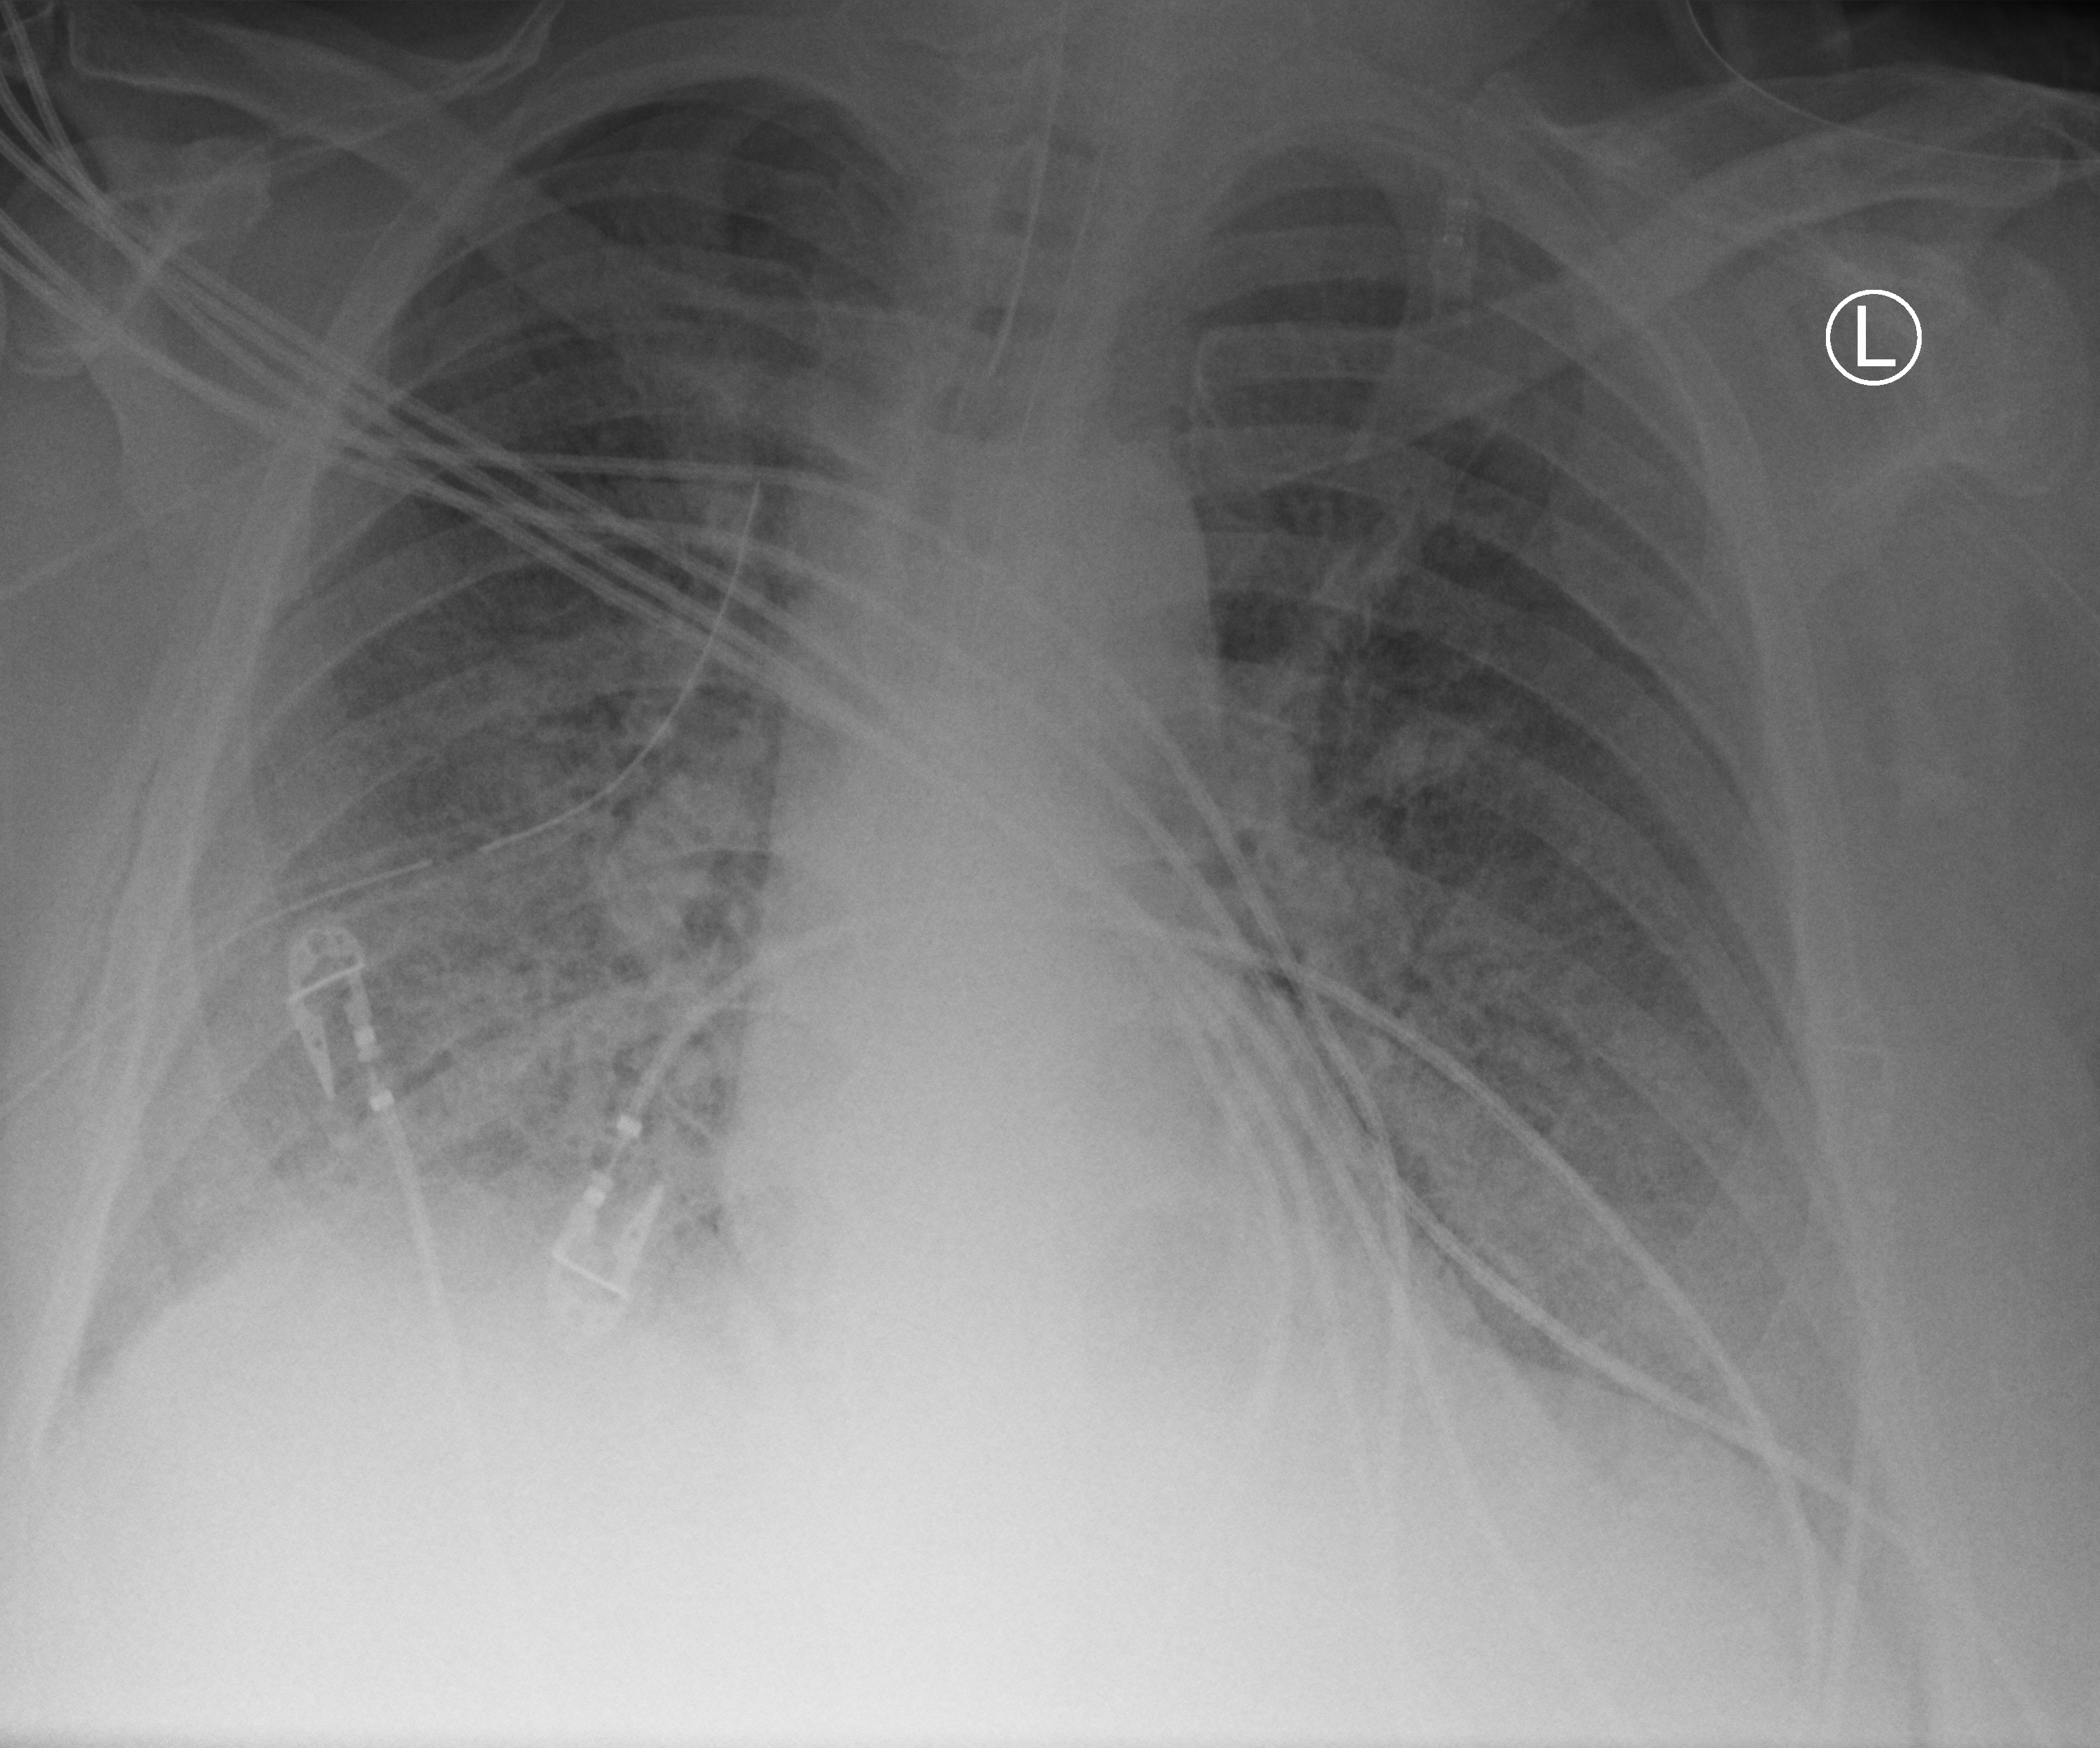
Bedside chest radiograph (computed radiography); anteroposterior (AP) projection. Patient hospitalised with COVID-19, aged 18–59 years.
Hospital-stay facts (about this admission, not read from this image; timing relative to this image not recorded):
- length of hospital stay: 26 days
- mechanically ventilated during this hospital stay: yes
- admitted to intensive care during this hospital stay: yes